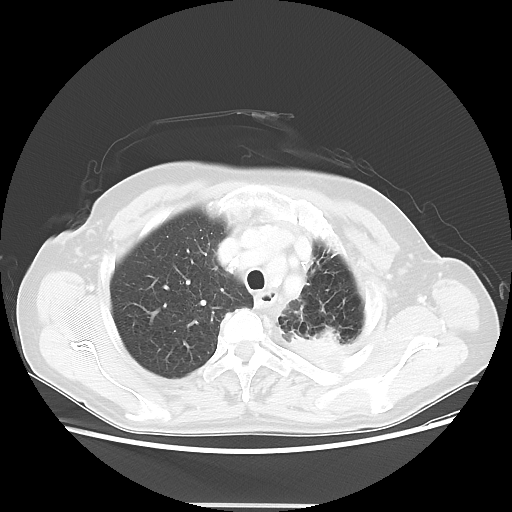
Chest CT, one axial slice. Position 43 of 56 along the scan axis. Reconstruction kernel LUNG. 100 kVp. Lung window (W 1500 / L -600 HU). 5 mm slice thickness. 512 × 512 image matrix, field of view 377 × 377 mm. Female patient, age 63 years. Case-level facts recorded for this patient, not image findings: clinical TNM (as recorded): T2a N0 M0.
Annotated regions visible in this slice (rectangle marked by the reading radiologist):
- lung tumour (recorded histology: adenocarcinoma): bounding box <302,313,344,352> (left, top, right, bottom; pixels)